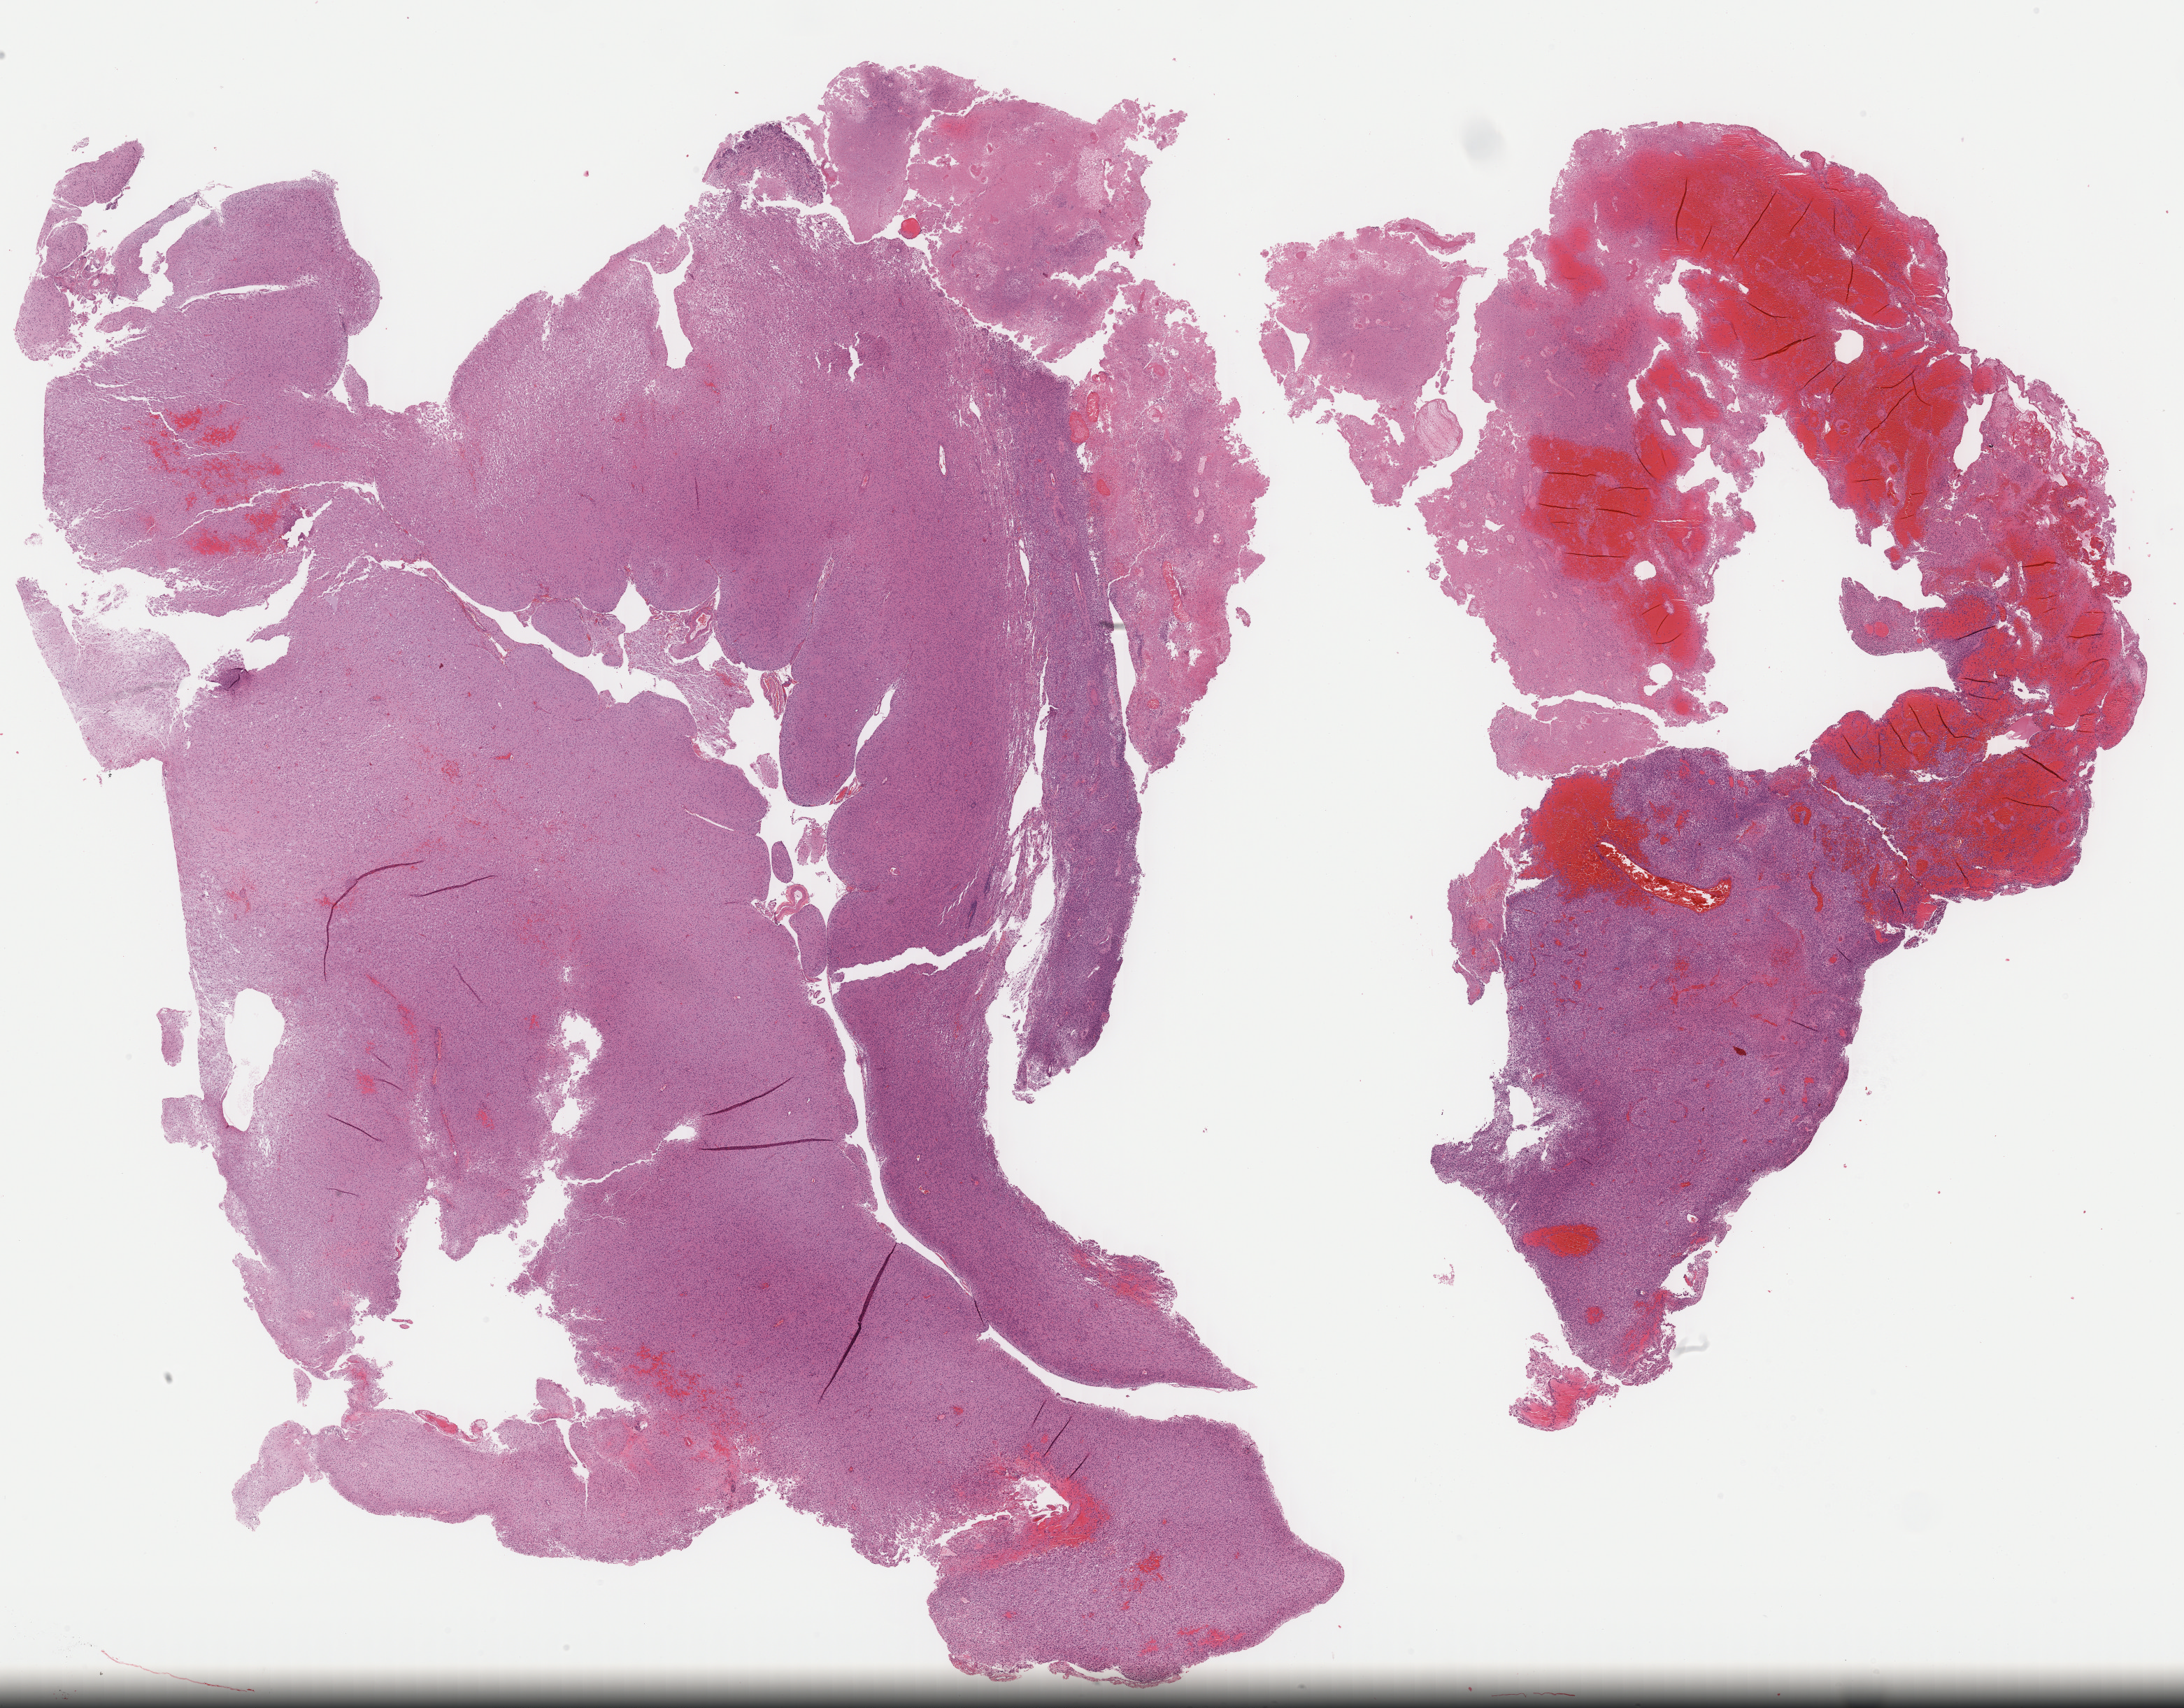
Hematoxylin and eosin (H&E) stained whole-slide image, low-resolution overview of the scanned area, about 24.6 x 19.2 mm (slide scanned at 40x). Formalin-fixed paraffin-embedded (FFPE) diagnostic section. Sample: primary tumour, brain. Male, age 55 years at initial diagnosis.
Pathologic diagnosis: Glioblastoma.